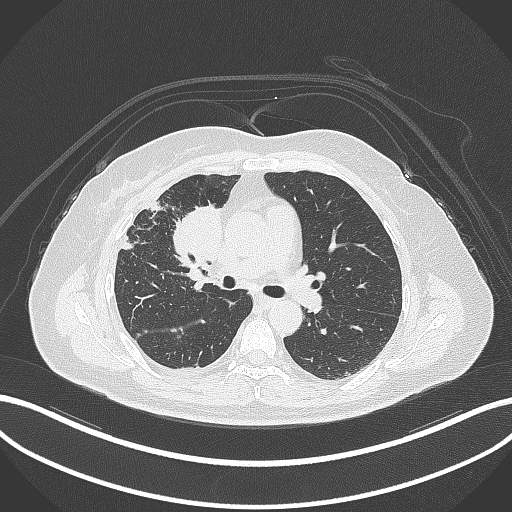
Chest CT, one axial slice; slice 166 of 305 in the series (ordered by position); lung window (W 1500 / L -600 HU); 1 mm slice thickness; 512 × 512 image matrix, field of view 400 × 400 mm. Patient: female, 52 years. Case-level facts recorded for this patient, not image findings: clinical TNM (as recorded): T3 N1 M1.
Annotated regions visible in this slice (bounding box drawn by a radiologist):
- lung tumour (recorded histology: adenocarcinoma): bounding box [x1, y1, x2, y2] px = [172, 199, 223, 266]